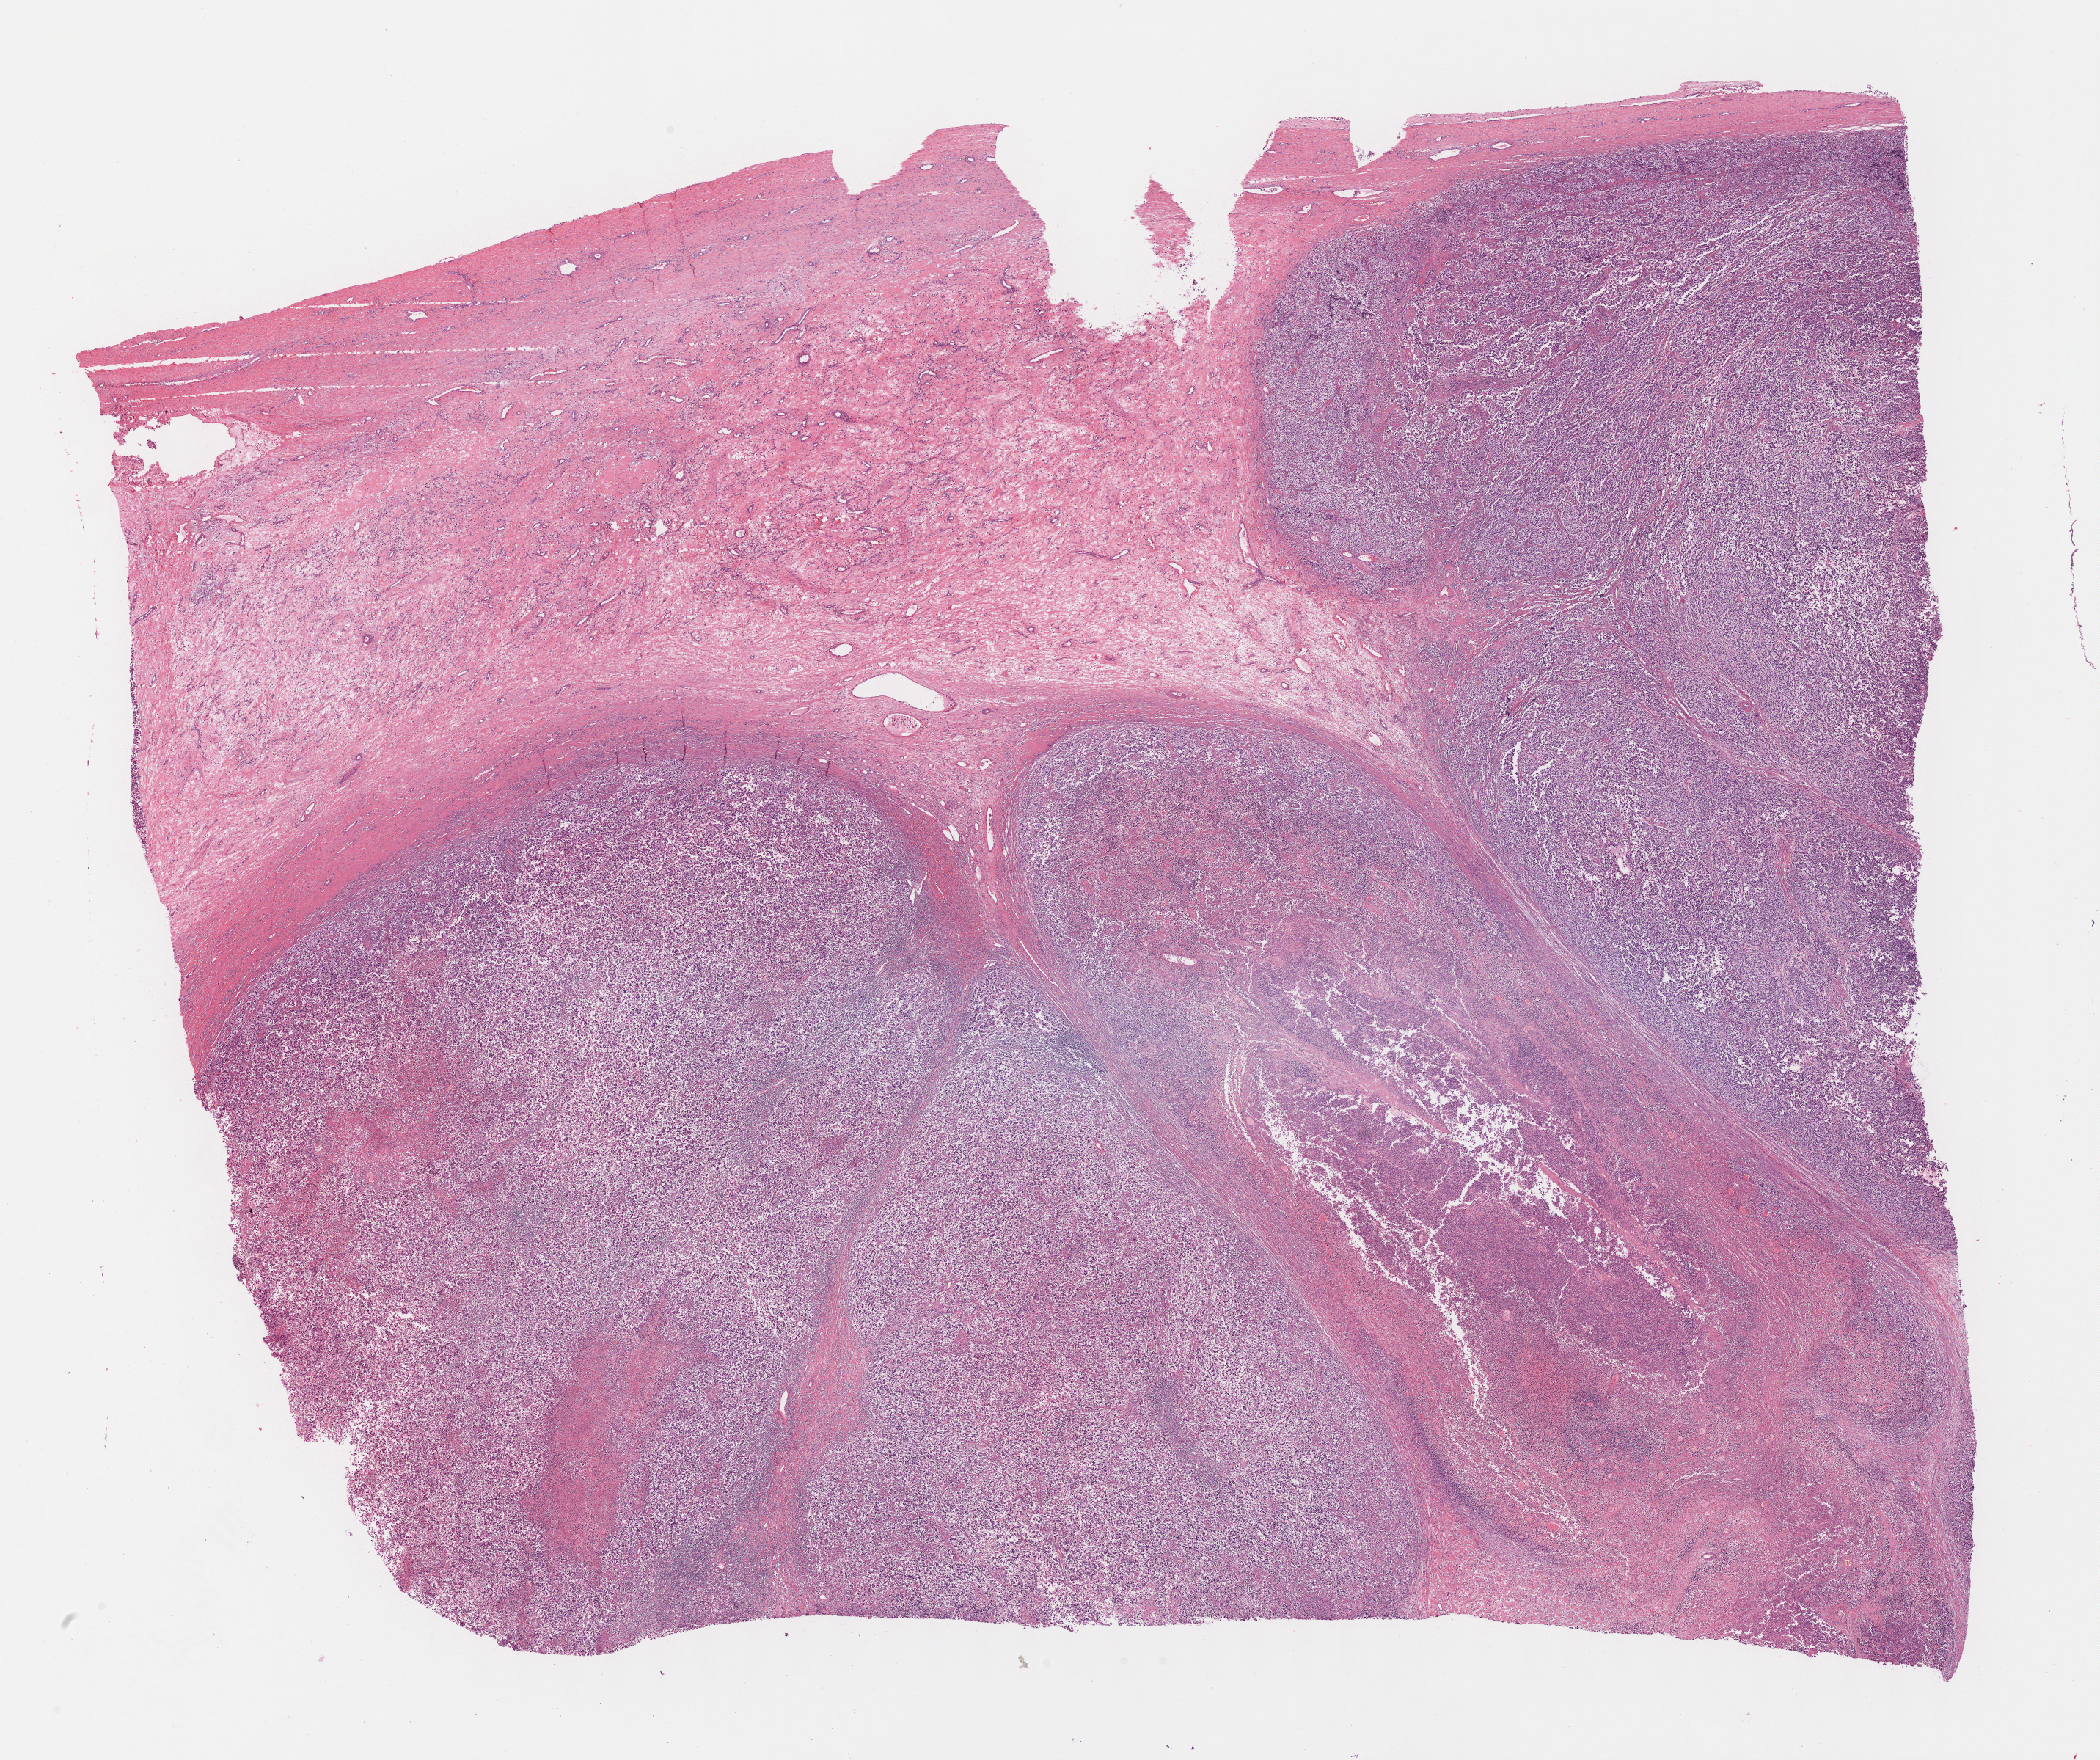
Whole-slide histology image, H&E, shown as a low-resolution overview of the whole scanned area (about 23.1 x 19.4 mm); formalin-fixed paraffin-embedded (FFPE) diagnostic section; testis, primary tumour sample. Male, age 23 years at initial diagnosis.
Diagnosis: Seminoma, NOS. TNM: T2 NX M0. AJCC pathologic stage: I (6th edition).